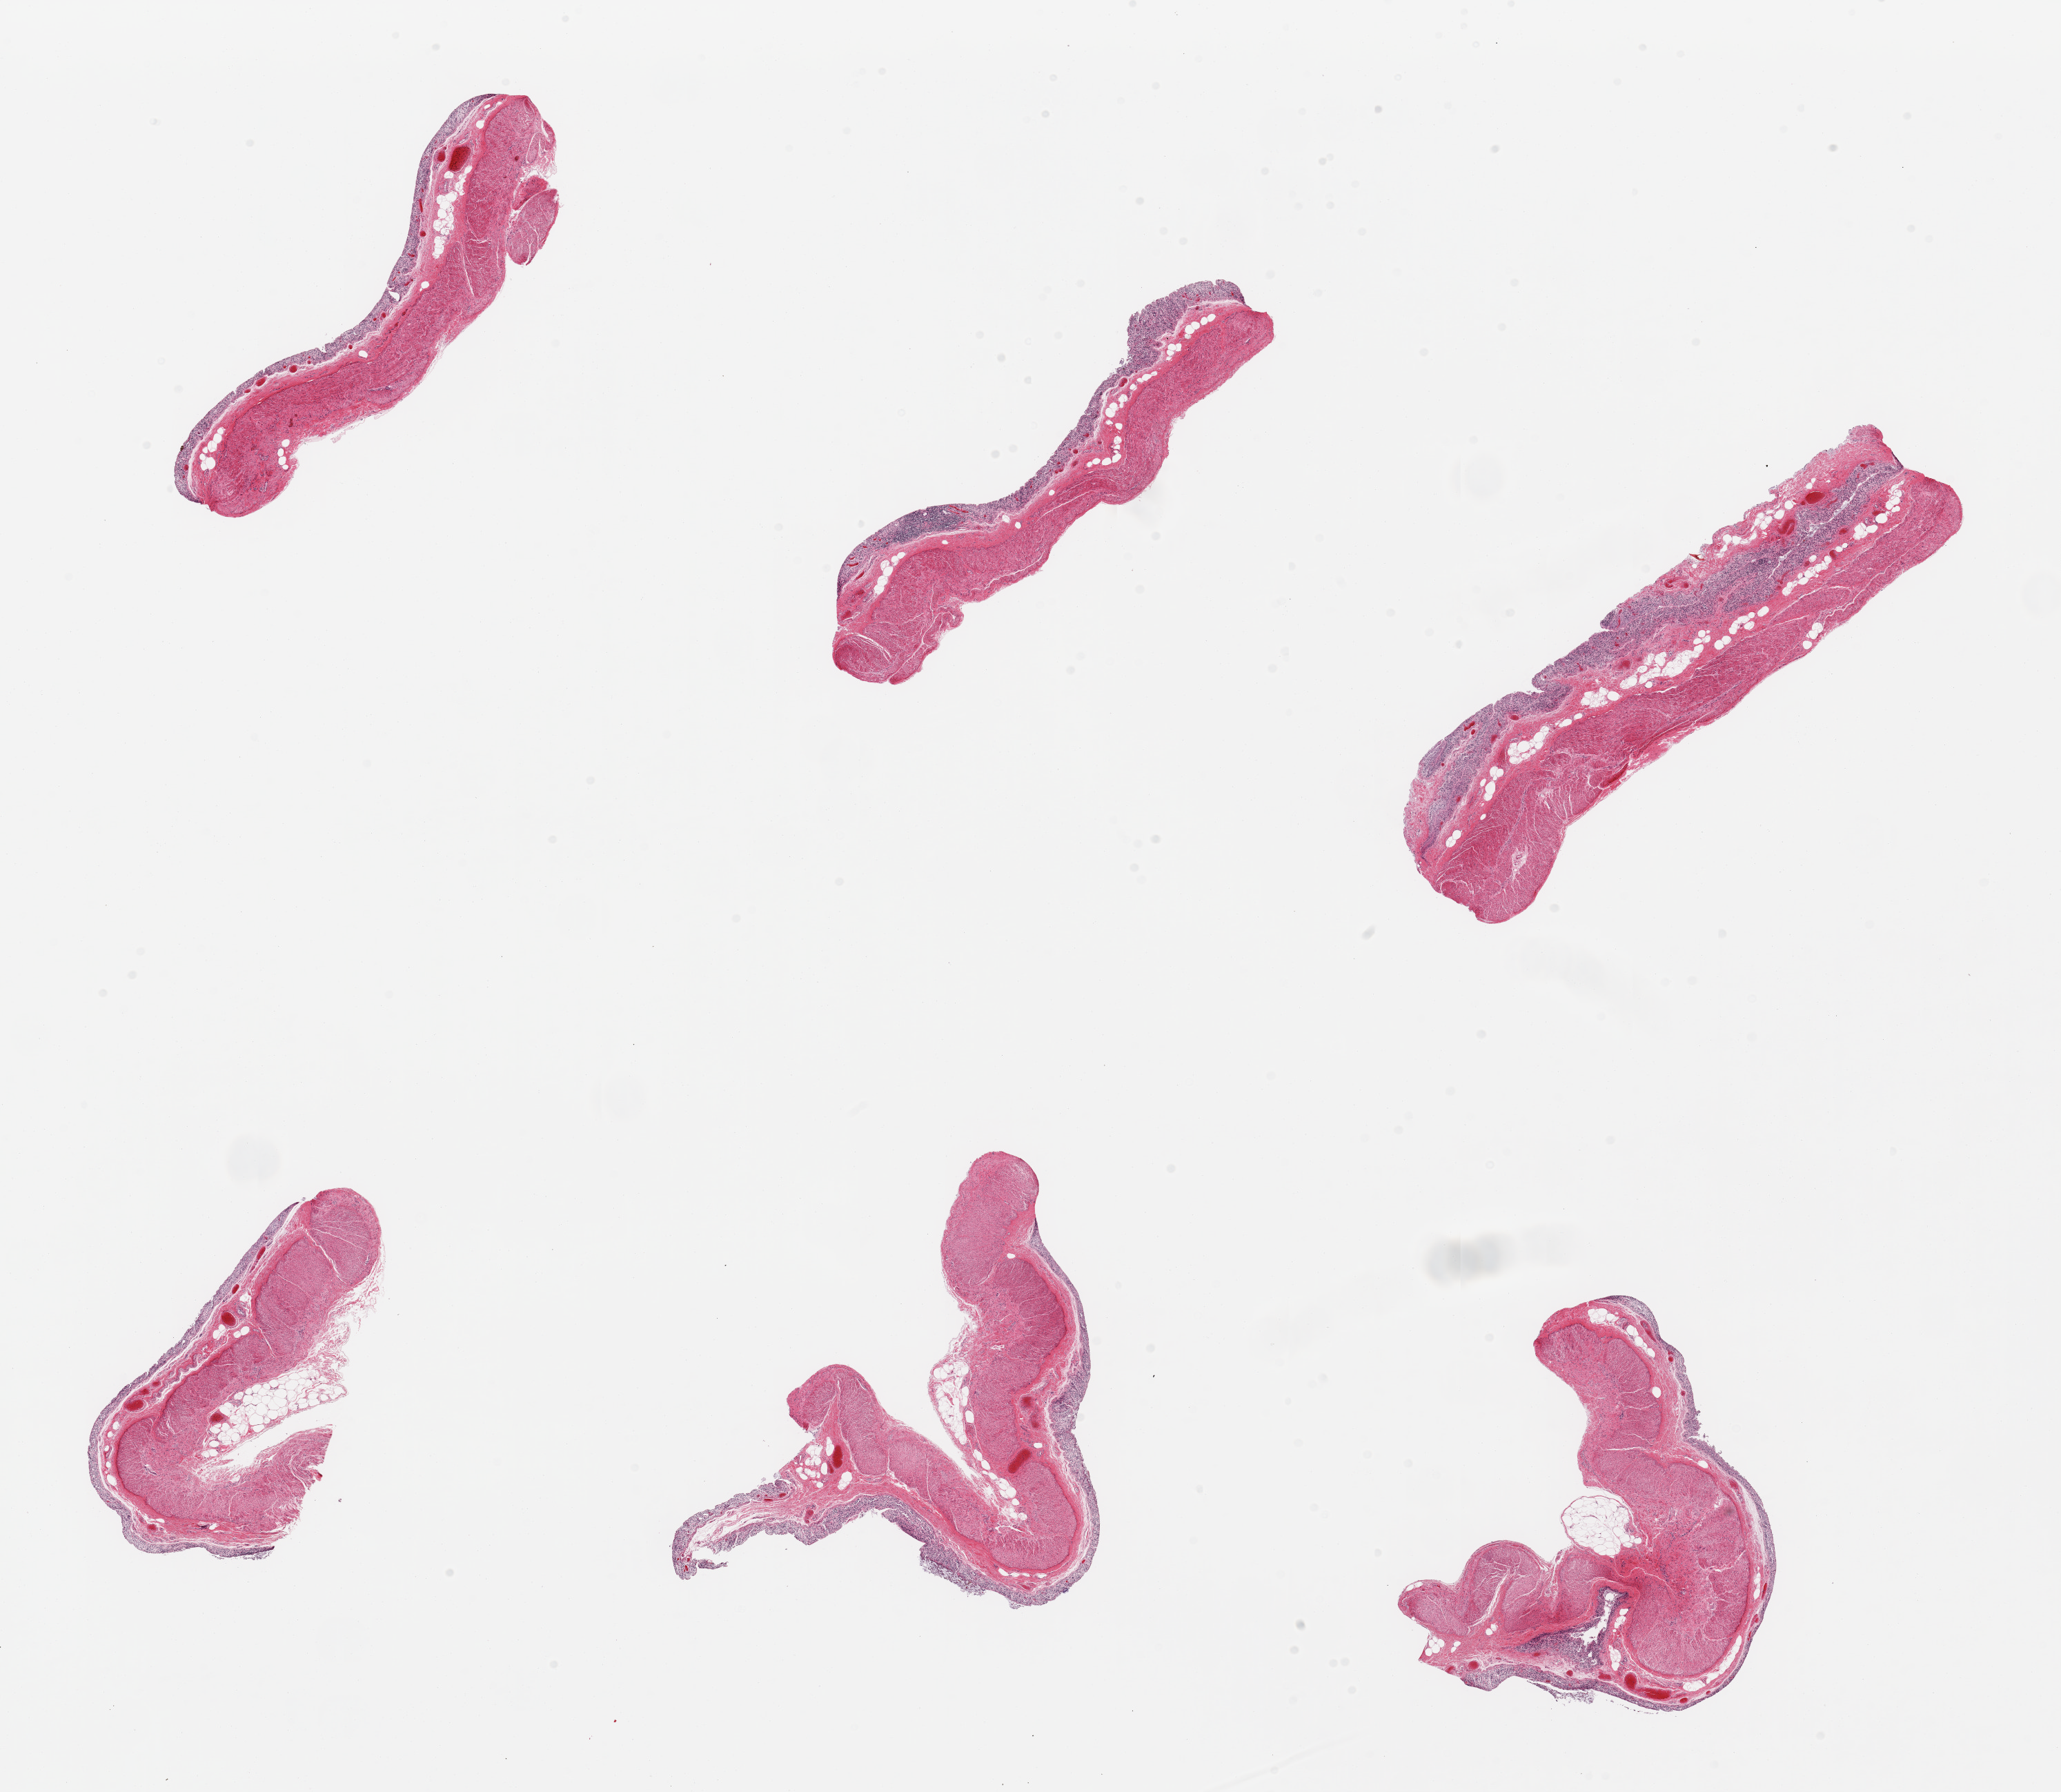
Digitized hematoxylin and eosin (H&E)-stained section, brightfield — whole scanned area (about 23.6 x 20.5 mm, slide scanned at 20x) shown as a low-resolution overview, PAXgene-fixed, paraffin-embedded tissue, sampled site (target tissue): transverse colon, tissue donor sample. Donor: male.
Review note (as recorded): 6 pieces, mucosa totally autolyzed.